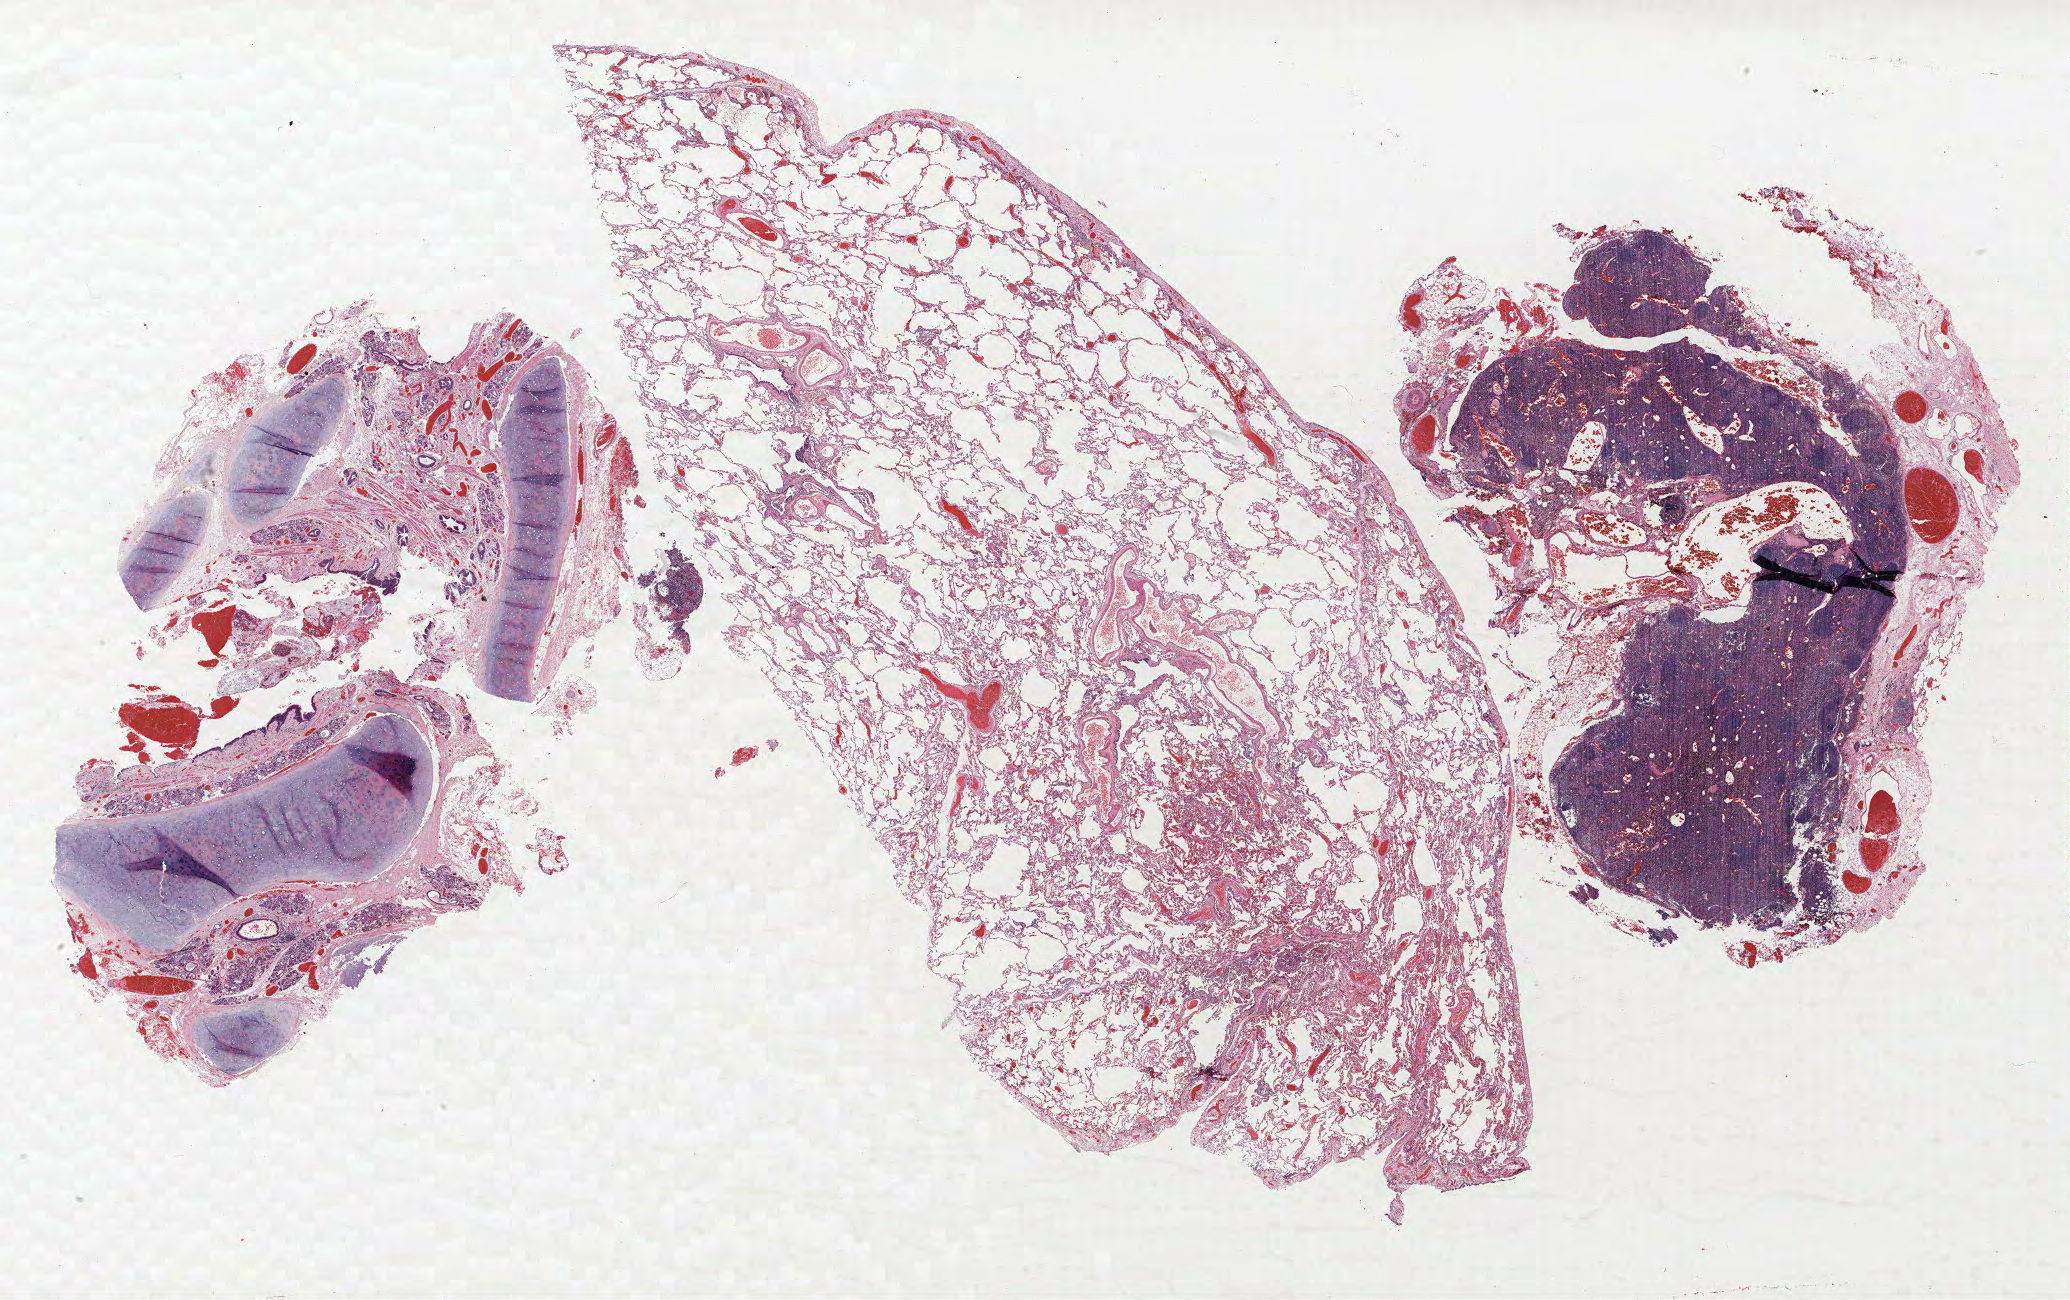
Whole-slide histology image, H&E-stained, a low-resolution overview of the entire scanned area, about 33.1 x 20.8 mm (acquisition: 40x scan), FFPE section, lung tissue. Male patient, aged 64 at enrolment. Grade: poorly differentiated (G3).
Participant's lung-cancer diagnosis: Adenocarcinoma, NOS. Primary tumour location (clinical record): left upper lobe. Tumour size (pathology): 10 mm. ICD-O-3 topography: upper lobe of lung (C34.1). Stage (AJCC 6th edition): IA.